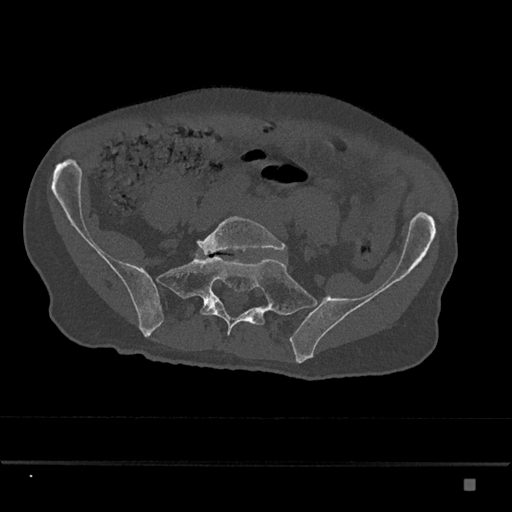
CT including the spine, one axial slice. Position 233 of 797 along the scan axis. Reconstruction kernel Br40s/3. Bone window (W 1800 / L 400 HU). 0.5 mm slice thickness. 512 × 512 image matrix. Patient: male, 72 years. Case-level facts recorded for this patient, not image findings: primary cancer: prostate.
Outlined on this slice (semi-automatic segmentation, software-assisted and operator-edited):
- L5 vertebra: bounding box [x1, y1, x2, y2] px = [197, 216, 286, 255]